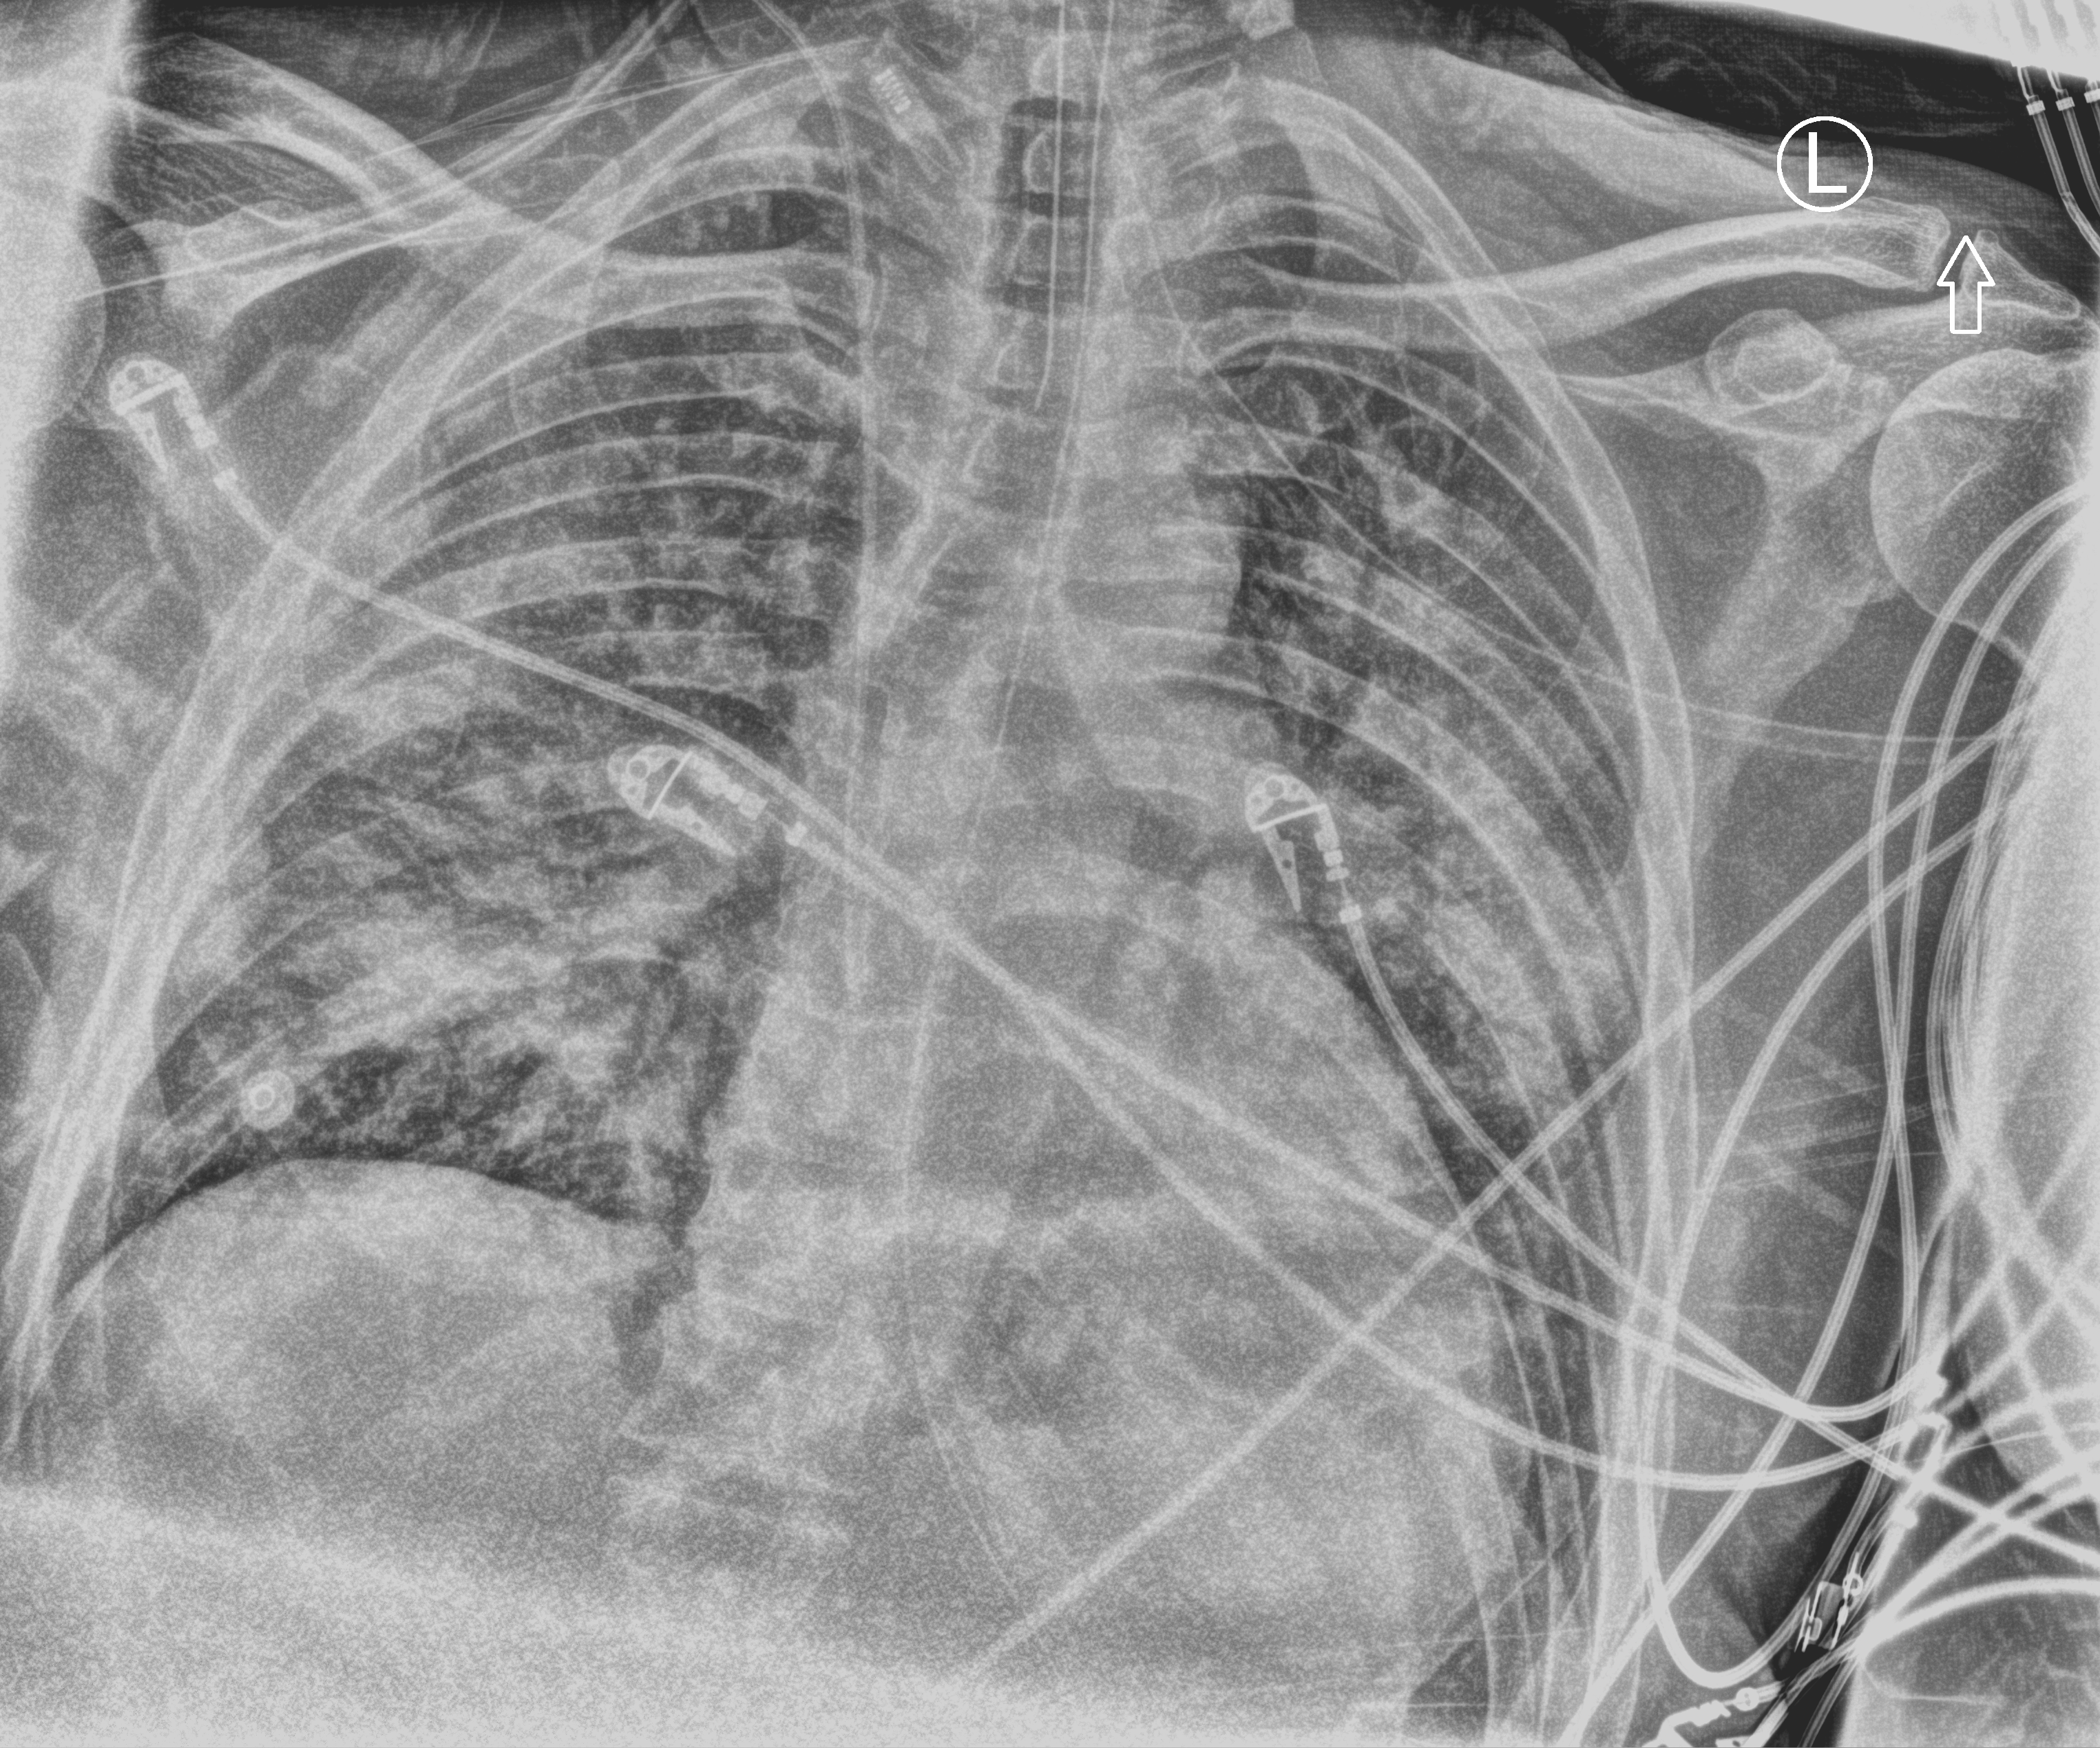
Portable chest radiograph. Patient hospitalised with COVID-19; male, aged 18–59 years.
From the hospital-stay record, not from the radiograph (when in the stay this image was taken is not recorded):
- mechanically ventilated during this hospital stay: yes
- COPD (admission record): no